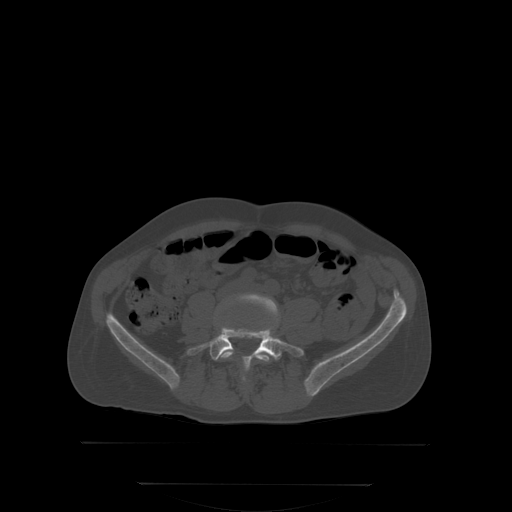
CT including the spine, one axial slice. Position 100 of 350 along the scan axis. Bone window (W 1800 / L 400 HU). 2.5 mm slice thickness. 512 × 512 image matrix, field of view 500 × 500 mm. Patient: male, 58 years. Case-level facts recorded for this patient, not image findings: primary cancer: prostate.
Structures marked on this image (semi-automatically segmented with operator editing):
- L4 vertebra: bounding box <218,294,277,362> (left, top, right, bottom; pixels)
- L5 vertebra: <187,327,303,380>